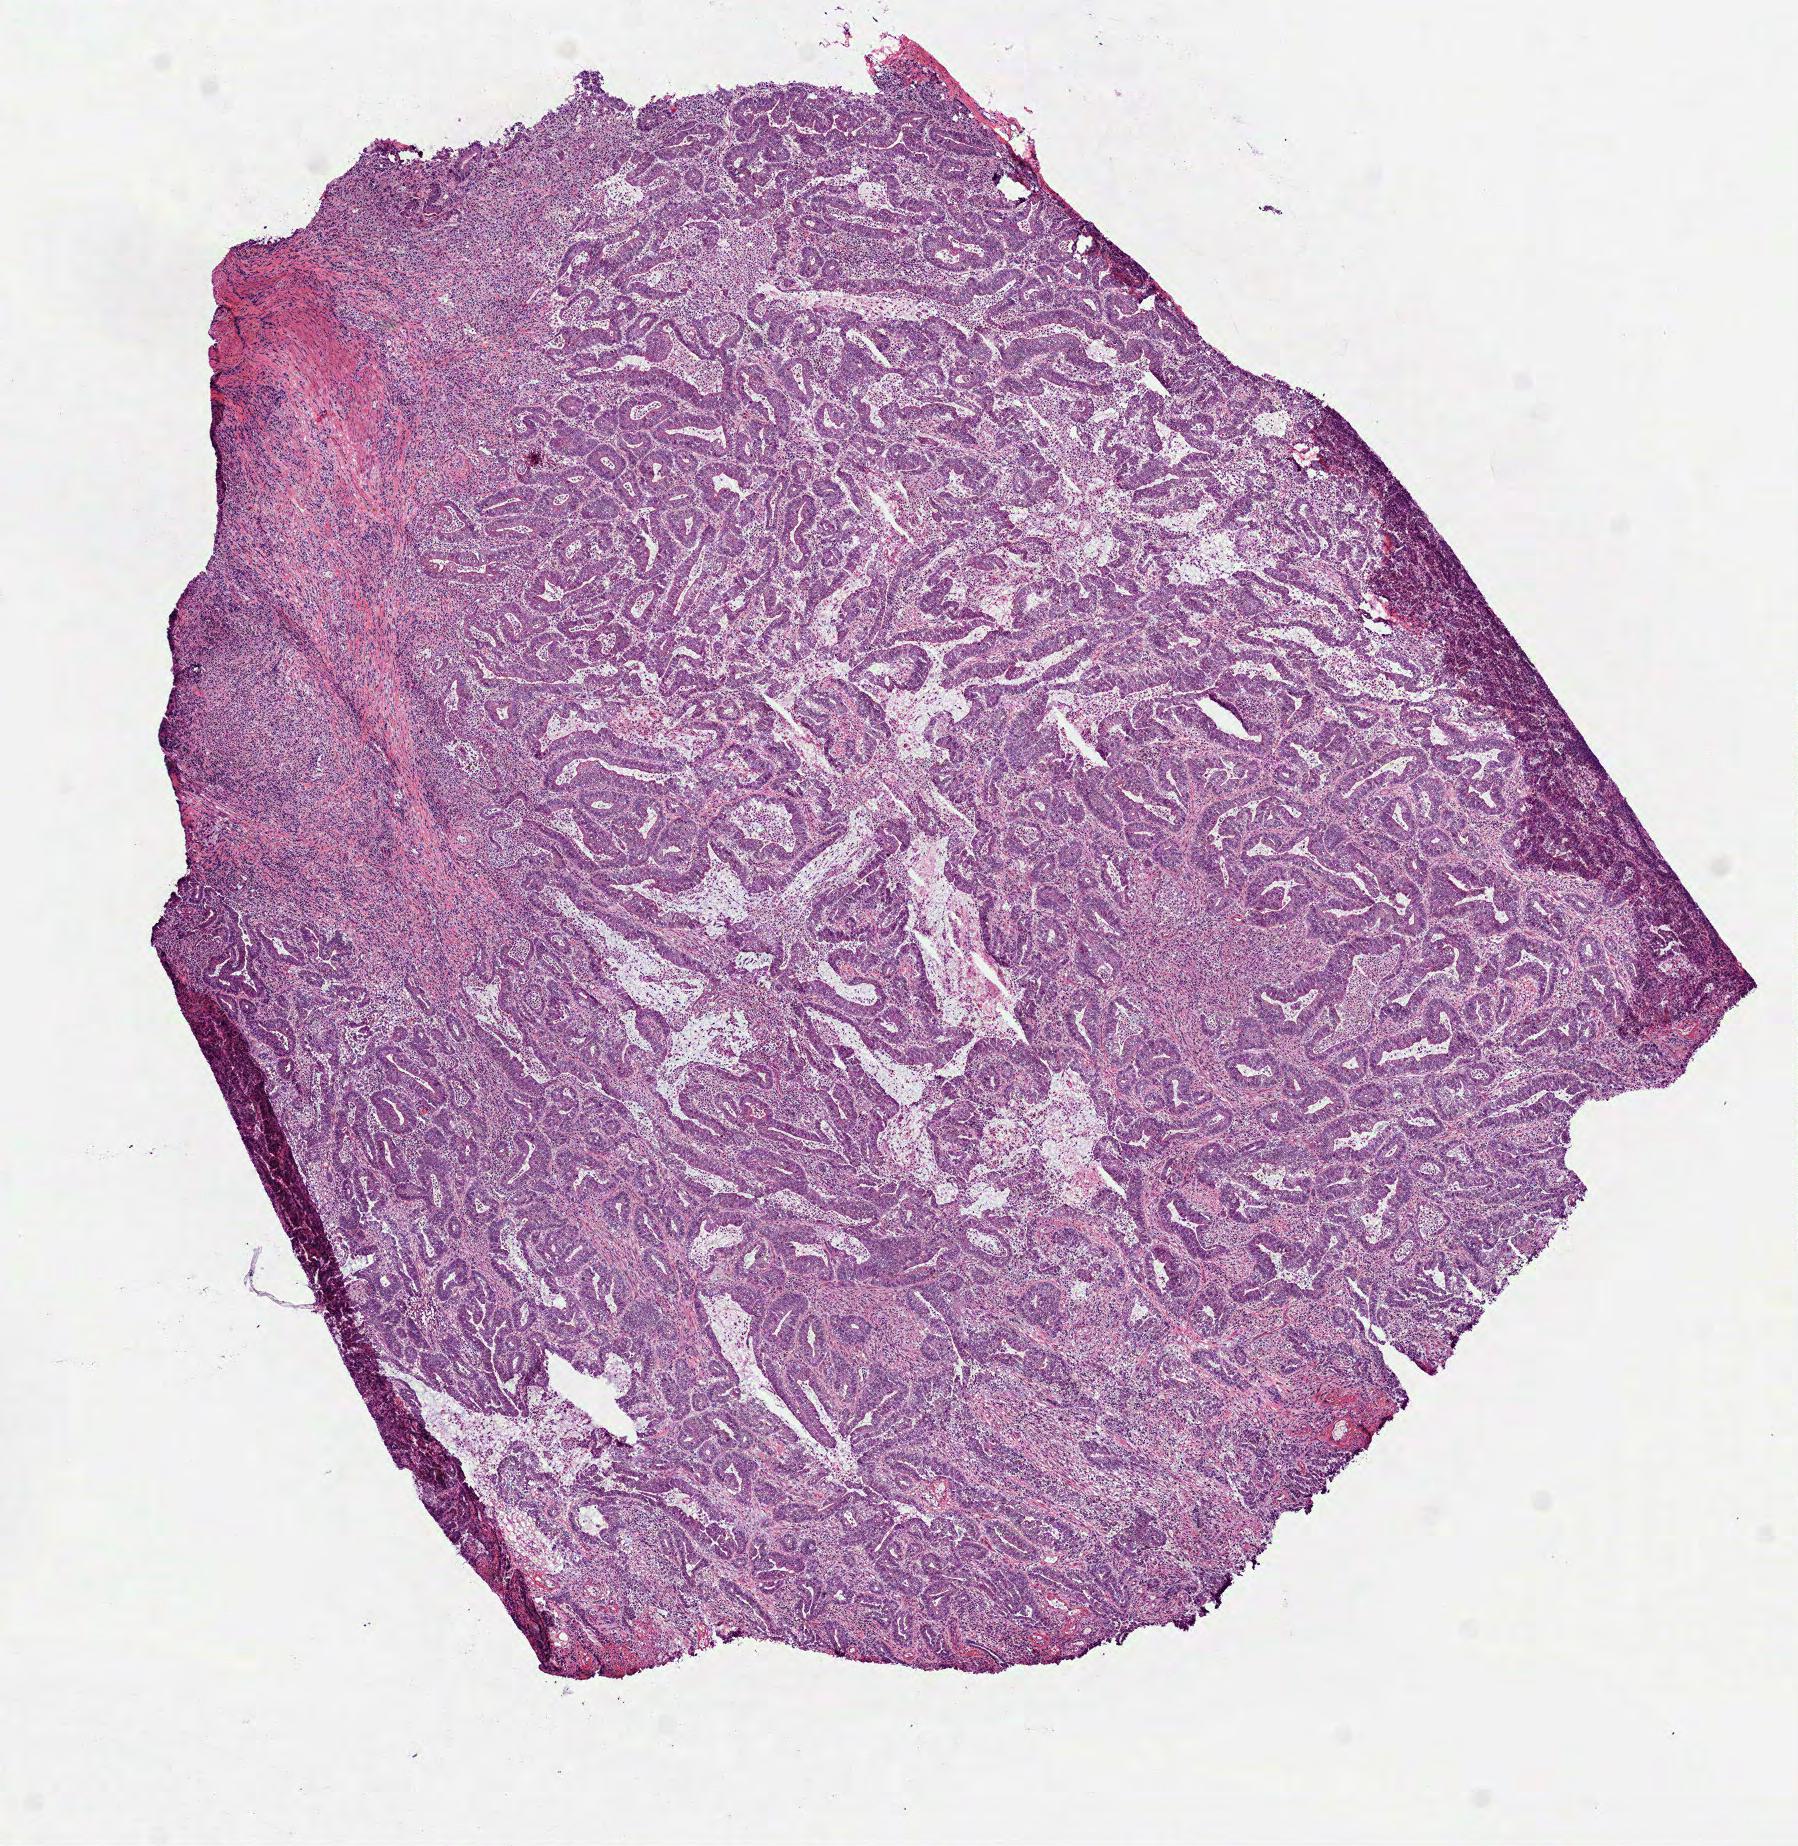
Digitized H&E tissue section (whole slide) — whole scanned area (about 7.3 x 7.4 mm) shown as a low-resolution overview, frozen section from the top of the tissue portion, sample: primary tumour, rectum. Male patient; age at initial diagnosis 73 years. Slide review estimates, as recorded: tumour cells 85%, tumour nuclei 75%, normal cells 0%, stromal cells 10%, necrosis 5%.
AJCC pathologic stage: IIIB. Pathologic diagnosis: Adenocarcinoma, NOS. Lymph nodes positive (case pathology): 0 of 11 examined.